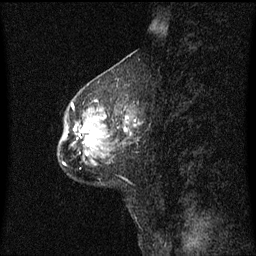
Breast MRI (dynamic contrast-enhanced), one sagittal slice; slice 21 of 60 in the series (ordered by position); dynamic contrast-enhanced series, image 2 of 3 at this slice position (ordered by acquisition); 1.5 T; TE 4.2 ms, TR 8.4 ms; 256 × 256 image matrix, field of view 200 × 200 mm. Female patient, age 49 years. Case-level facts recorded for this patient, not image findings: setting: breast cancer imaged before/during neoadjuvant chemotherapy; receptor status: HR-positive, HER2-negative.
Outlined on this slice (semi-automatic segmentation, software-assisted and operator-edited):
- analysis volume of interest (the breast-tissue region the enhancement analysis was run in; not a lesion): box from (x=59, y=106) to (x=136, y=158) px
- tumour enhancement mask (voxels above the 70 % enhancement threshold inside the analysis volume of interest): (x=80, y=117)–(x=129, y=146)